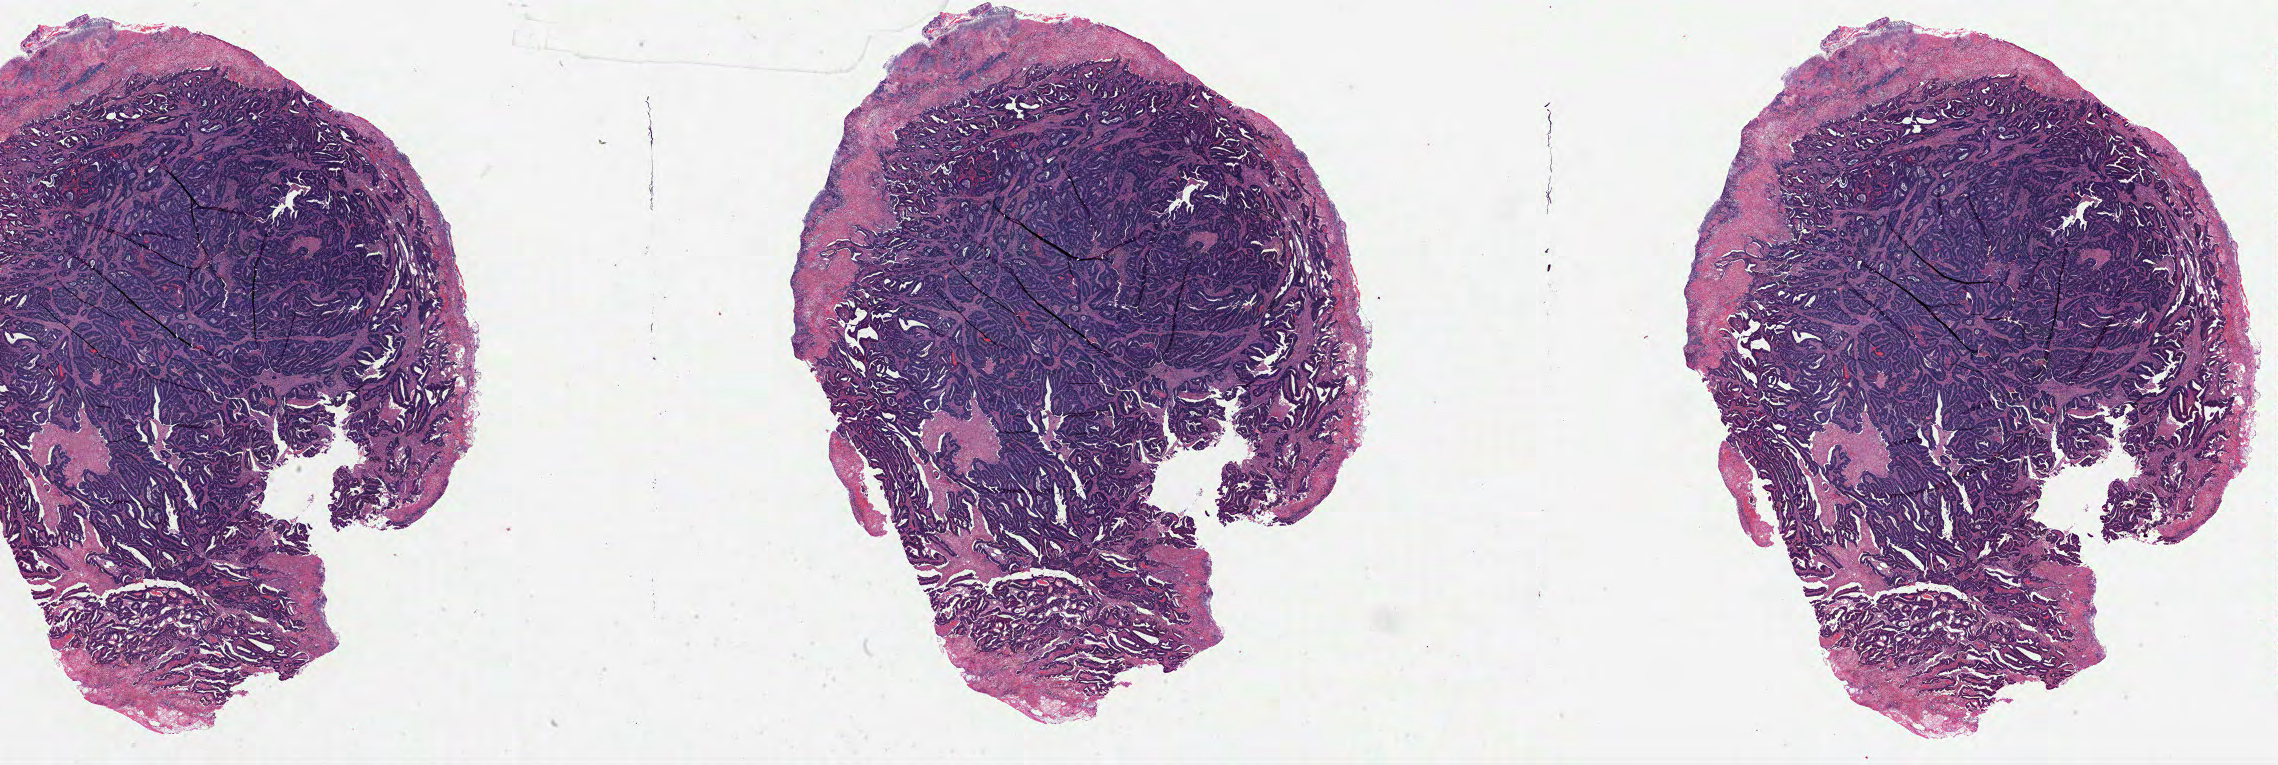
Whole-slide histology image, H&E-stained — a low-resolution overview of the entire scanned area, about 36.7 x 12.3 mm (slide scanned at 40x). Formalin-fixed paraffin-embedded (FFPE) diagnostic section. Stomach, primary tumour sample. Male patient. Histologic grade: G2 (moderately differentiated).
Pathologic diagnosis: Adenocarcinoma, NOS. AJCC pathologic stage: I (6th edition).